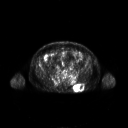
FDG PET of an extremity soft-tissue mass (from a PET/CT study), one axial slice. Slice 86 of 267 in the series (ordered by position). 128 × 128 image matrix, field of view 700 × 700 mm. Male patient, age 61 years. Case-level facts recorded for this patient, not image findings: histological type: pleiomorphic leiomyosarcoma; grade: high; site of the primary tumour: left buttock.
Structures marked on this image (expert contour drawn on MRI and transferred to this co-registered scan by the dataset authors):
- gross tumour volume including surrounding oedema: box from (x=73, y=83) to (x=84, y=91) px
- gross tumour volume (mass): (x=73, y=84)–(x=84, y=91)